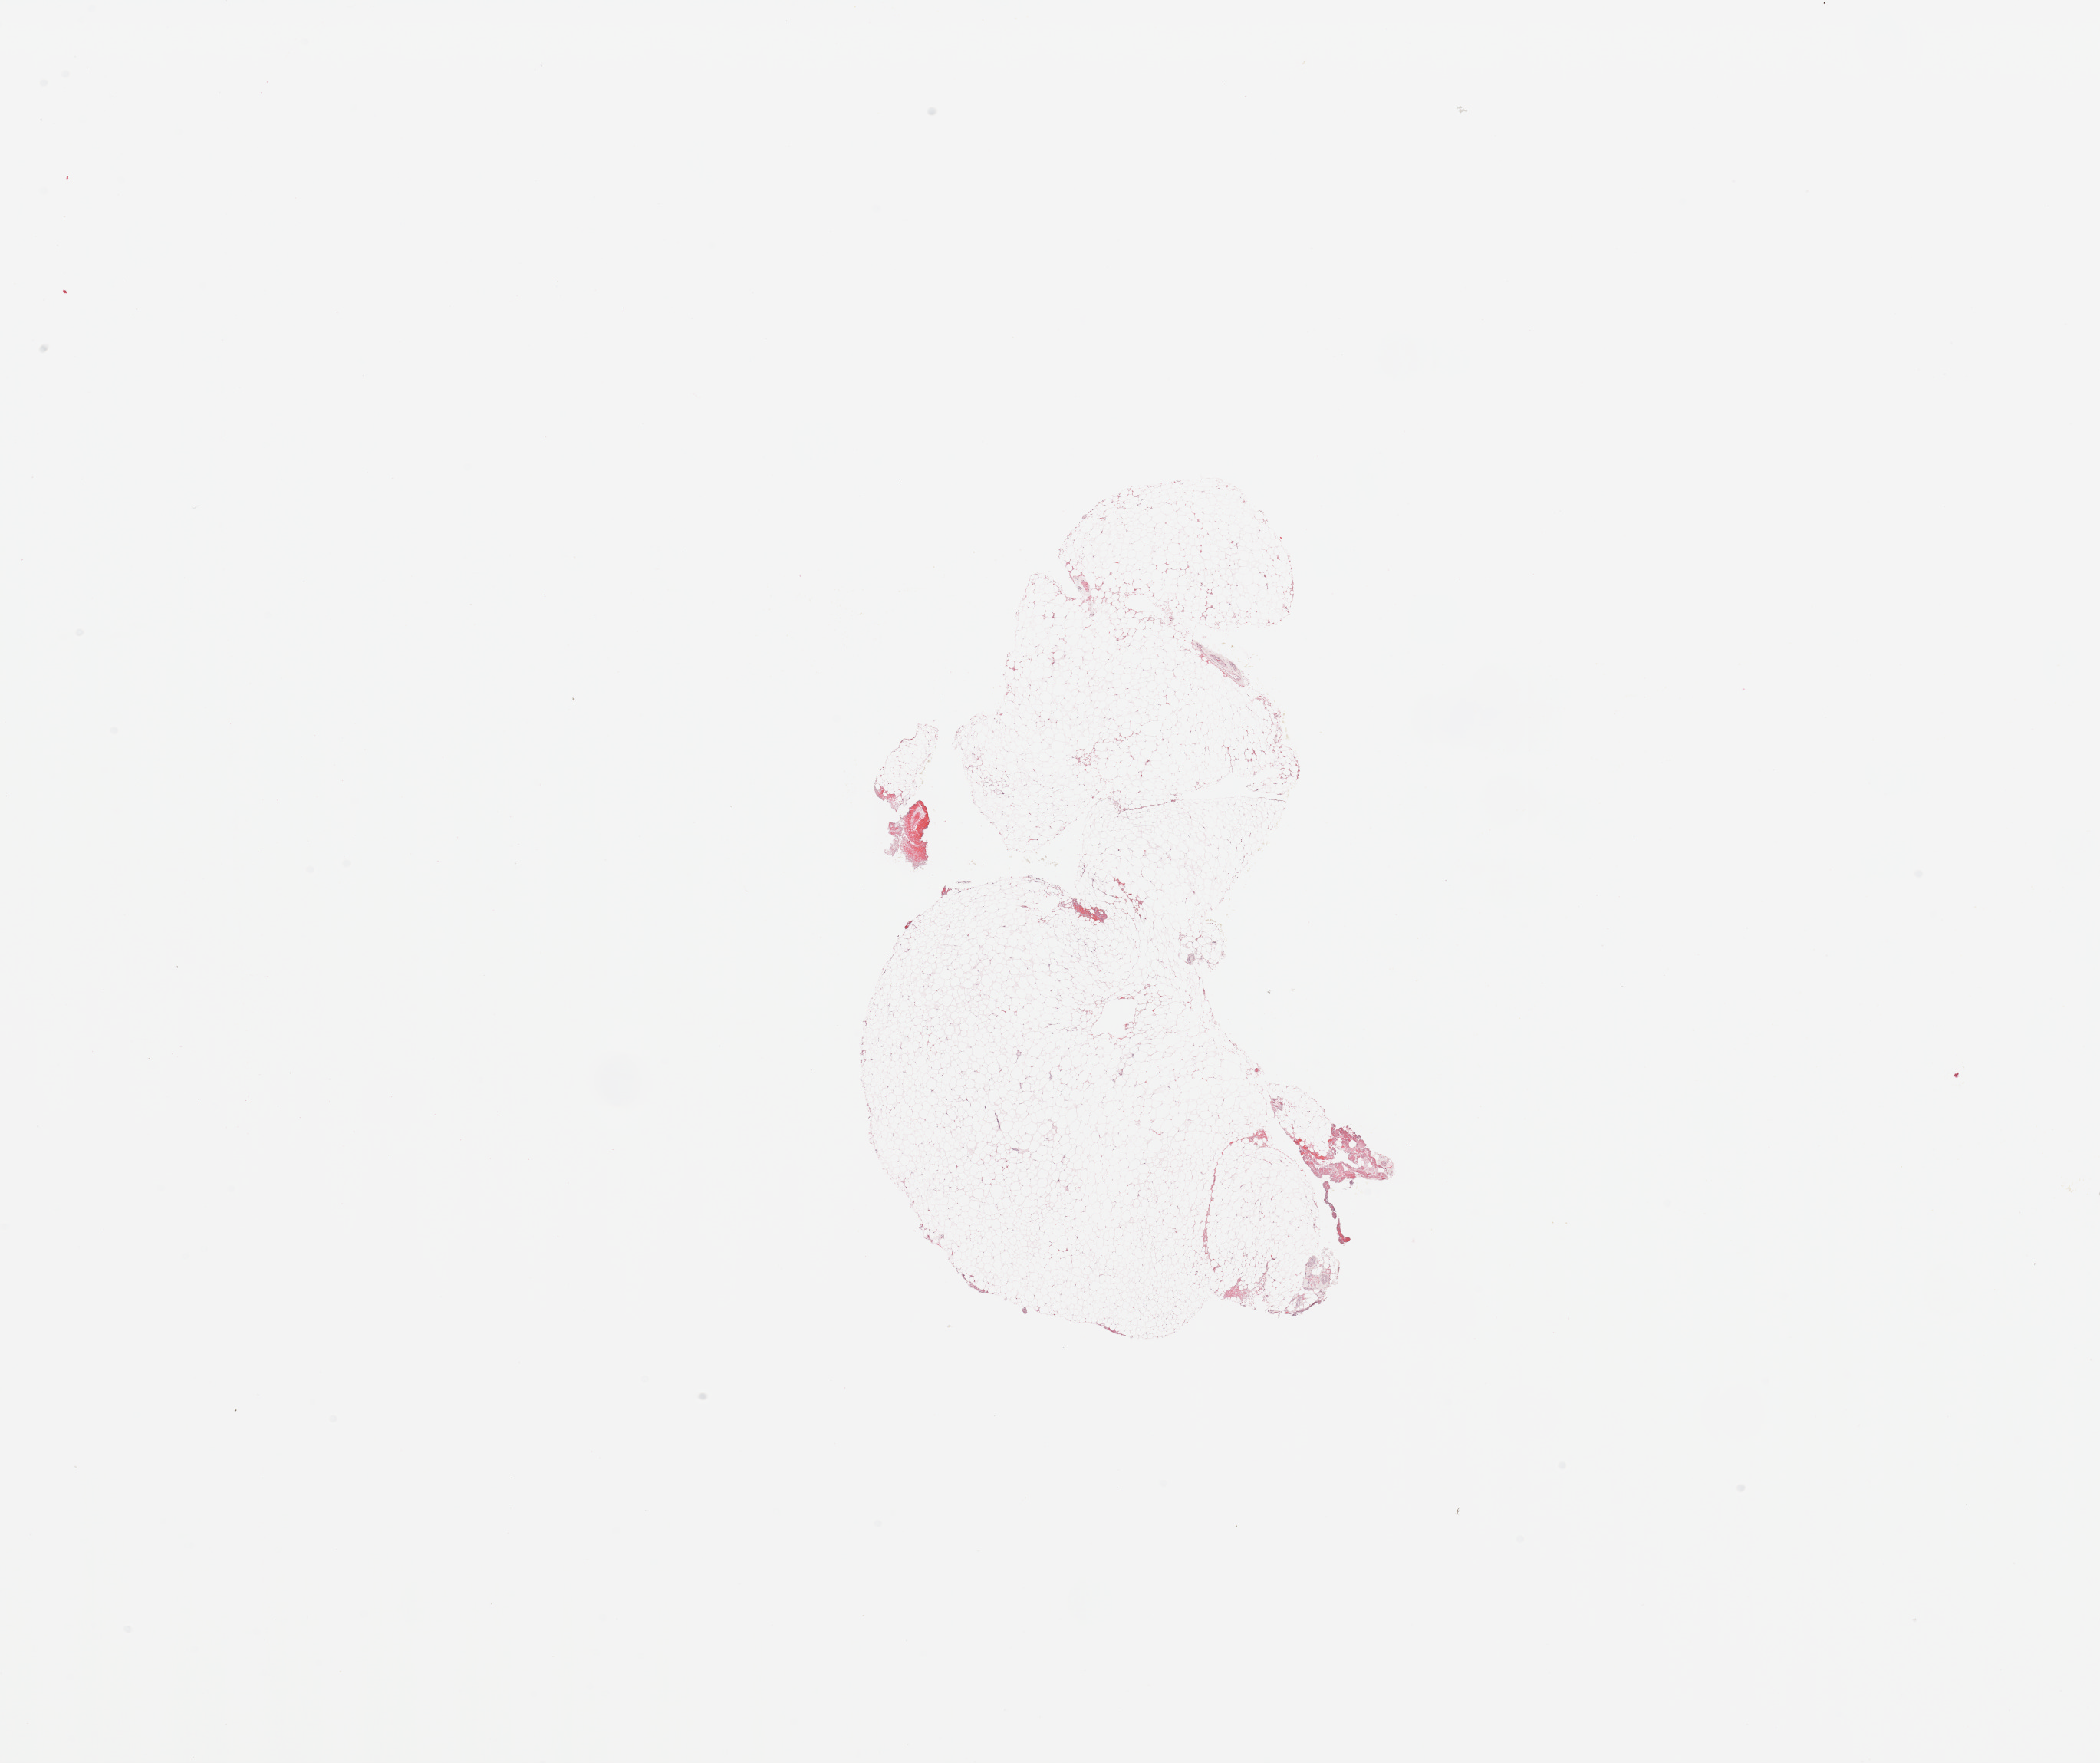
Digitized H&E tissue section (whole slide), a low-resolution overview of the entire scanned area, about 21.7 x 18.2 mm (from a 20x scan); kidney, normal (non-tumour) tissue. 61-year-old male patient.
* this section: normal (non-tumour) tissue from the same patient
* patient diagnosis: Renal cell carcinoma, NOS